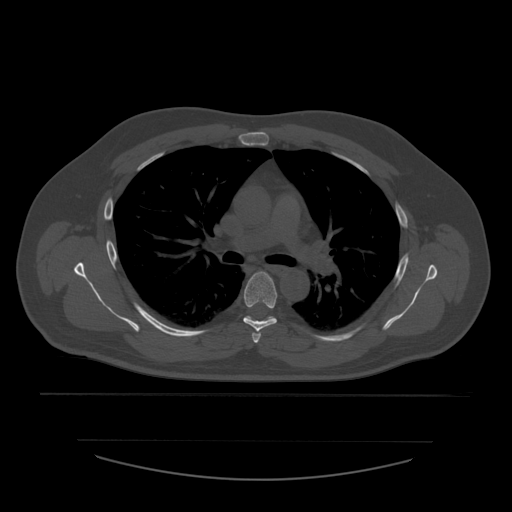
CT including the spine, one axial slice; position 397 of 532 along the scan axis; bone window (W 1800 / L 400 HU); 512 × 512 image matrix, field of view 441 × 441 mm. Patient age 44 years. Case-level facts recorded for this patient, not image findings: primary cancer: soft tissue sarcoma.
Structures marked on this image (semi-automatically segmented with operator editing):
- T4 vertebra: bounding box [x1, y1, x2, y2] px = [252, 332, 261, 343]
- T5 vertebra: [244, 272, 278, 332]
- T6 vertebra: [245, 316, 274, 321]